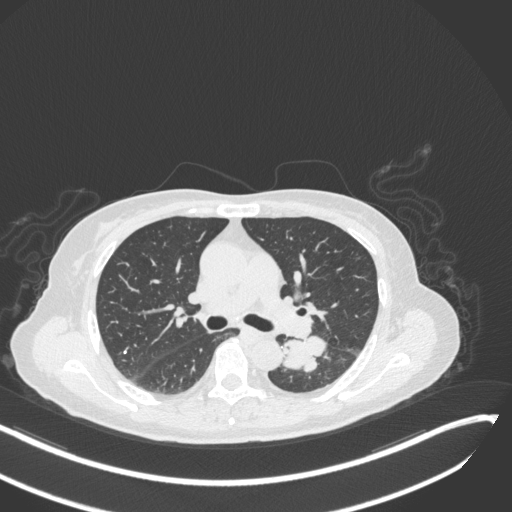
Chest CT, one axial slice; slice 172 of 342 in the series (ordered by position); lung window (W 1500 / L -600 HU); 1 mm slice thickness; 512 × 512 image matrix, field of view 400 × 400 mm. Female patient, age 64 years. From the clinical record (not read from this slice): clinical TNM (as recorded): T3 N1 M1.
Annotated regions visible in this slice (rectangle marked by the reading radiologist):
- lung tumour (recorded histology: small cell carcinoma): bounding box (x1, y1, x2, y2) in pixels: (276, 330, 329, 375)